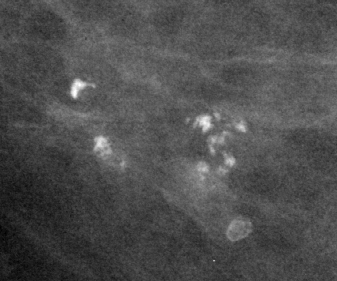
Crop from a digitized film mammogram around one marked abnormality; right breast; CC view.
- Calcifications, morphology pleomorphic, distribution clustered; BI-RADS assessment category 2; benign; no additional work-up was recommended (benign without callback).